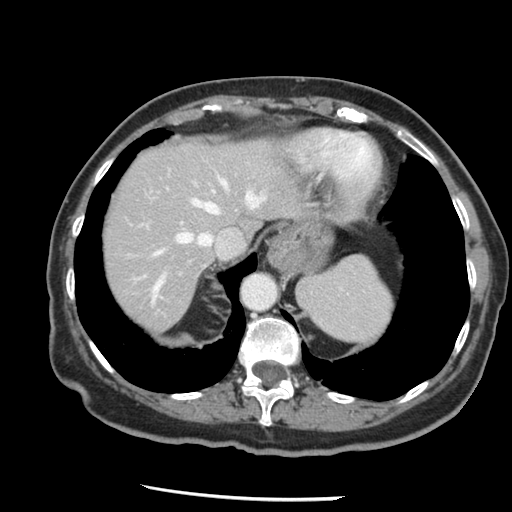
Contrast-enhanced abdominal CT, one axial slice; slice 110 of 148 in the series (ordered by position); reconstruction kernel STANDARD; 120 kVp; intravenous contrast given; soft-tissue window (W 400 / L 40 HU); 512 × 512 image matrix. Female patient, age 85 years. Case-level facts recorded for this patient, not image findings: diagnosis: colorectal cancer liver metastases, imaged before liver resection; multiple liver metastases: no; largest metastasis: 0.9 cm; chemotherapy before resection: yes.
Annotated regions visible in this slice (expert manual segmentation):
- hepatic veins: bounding box <152,162,266,303> (left, top, right, bottom; pixels)
- liver: <102,139,300,331>
- planned liver remnant (the part of the liver to remain after resection): <102,139,300,331>
- portal vein (with intrahepatic branches): <134,224,148,281>